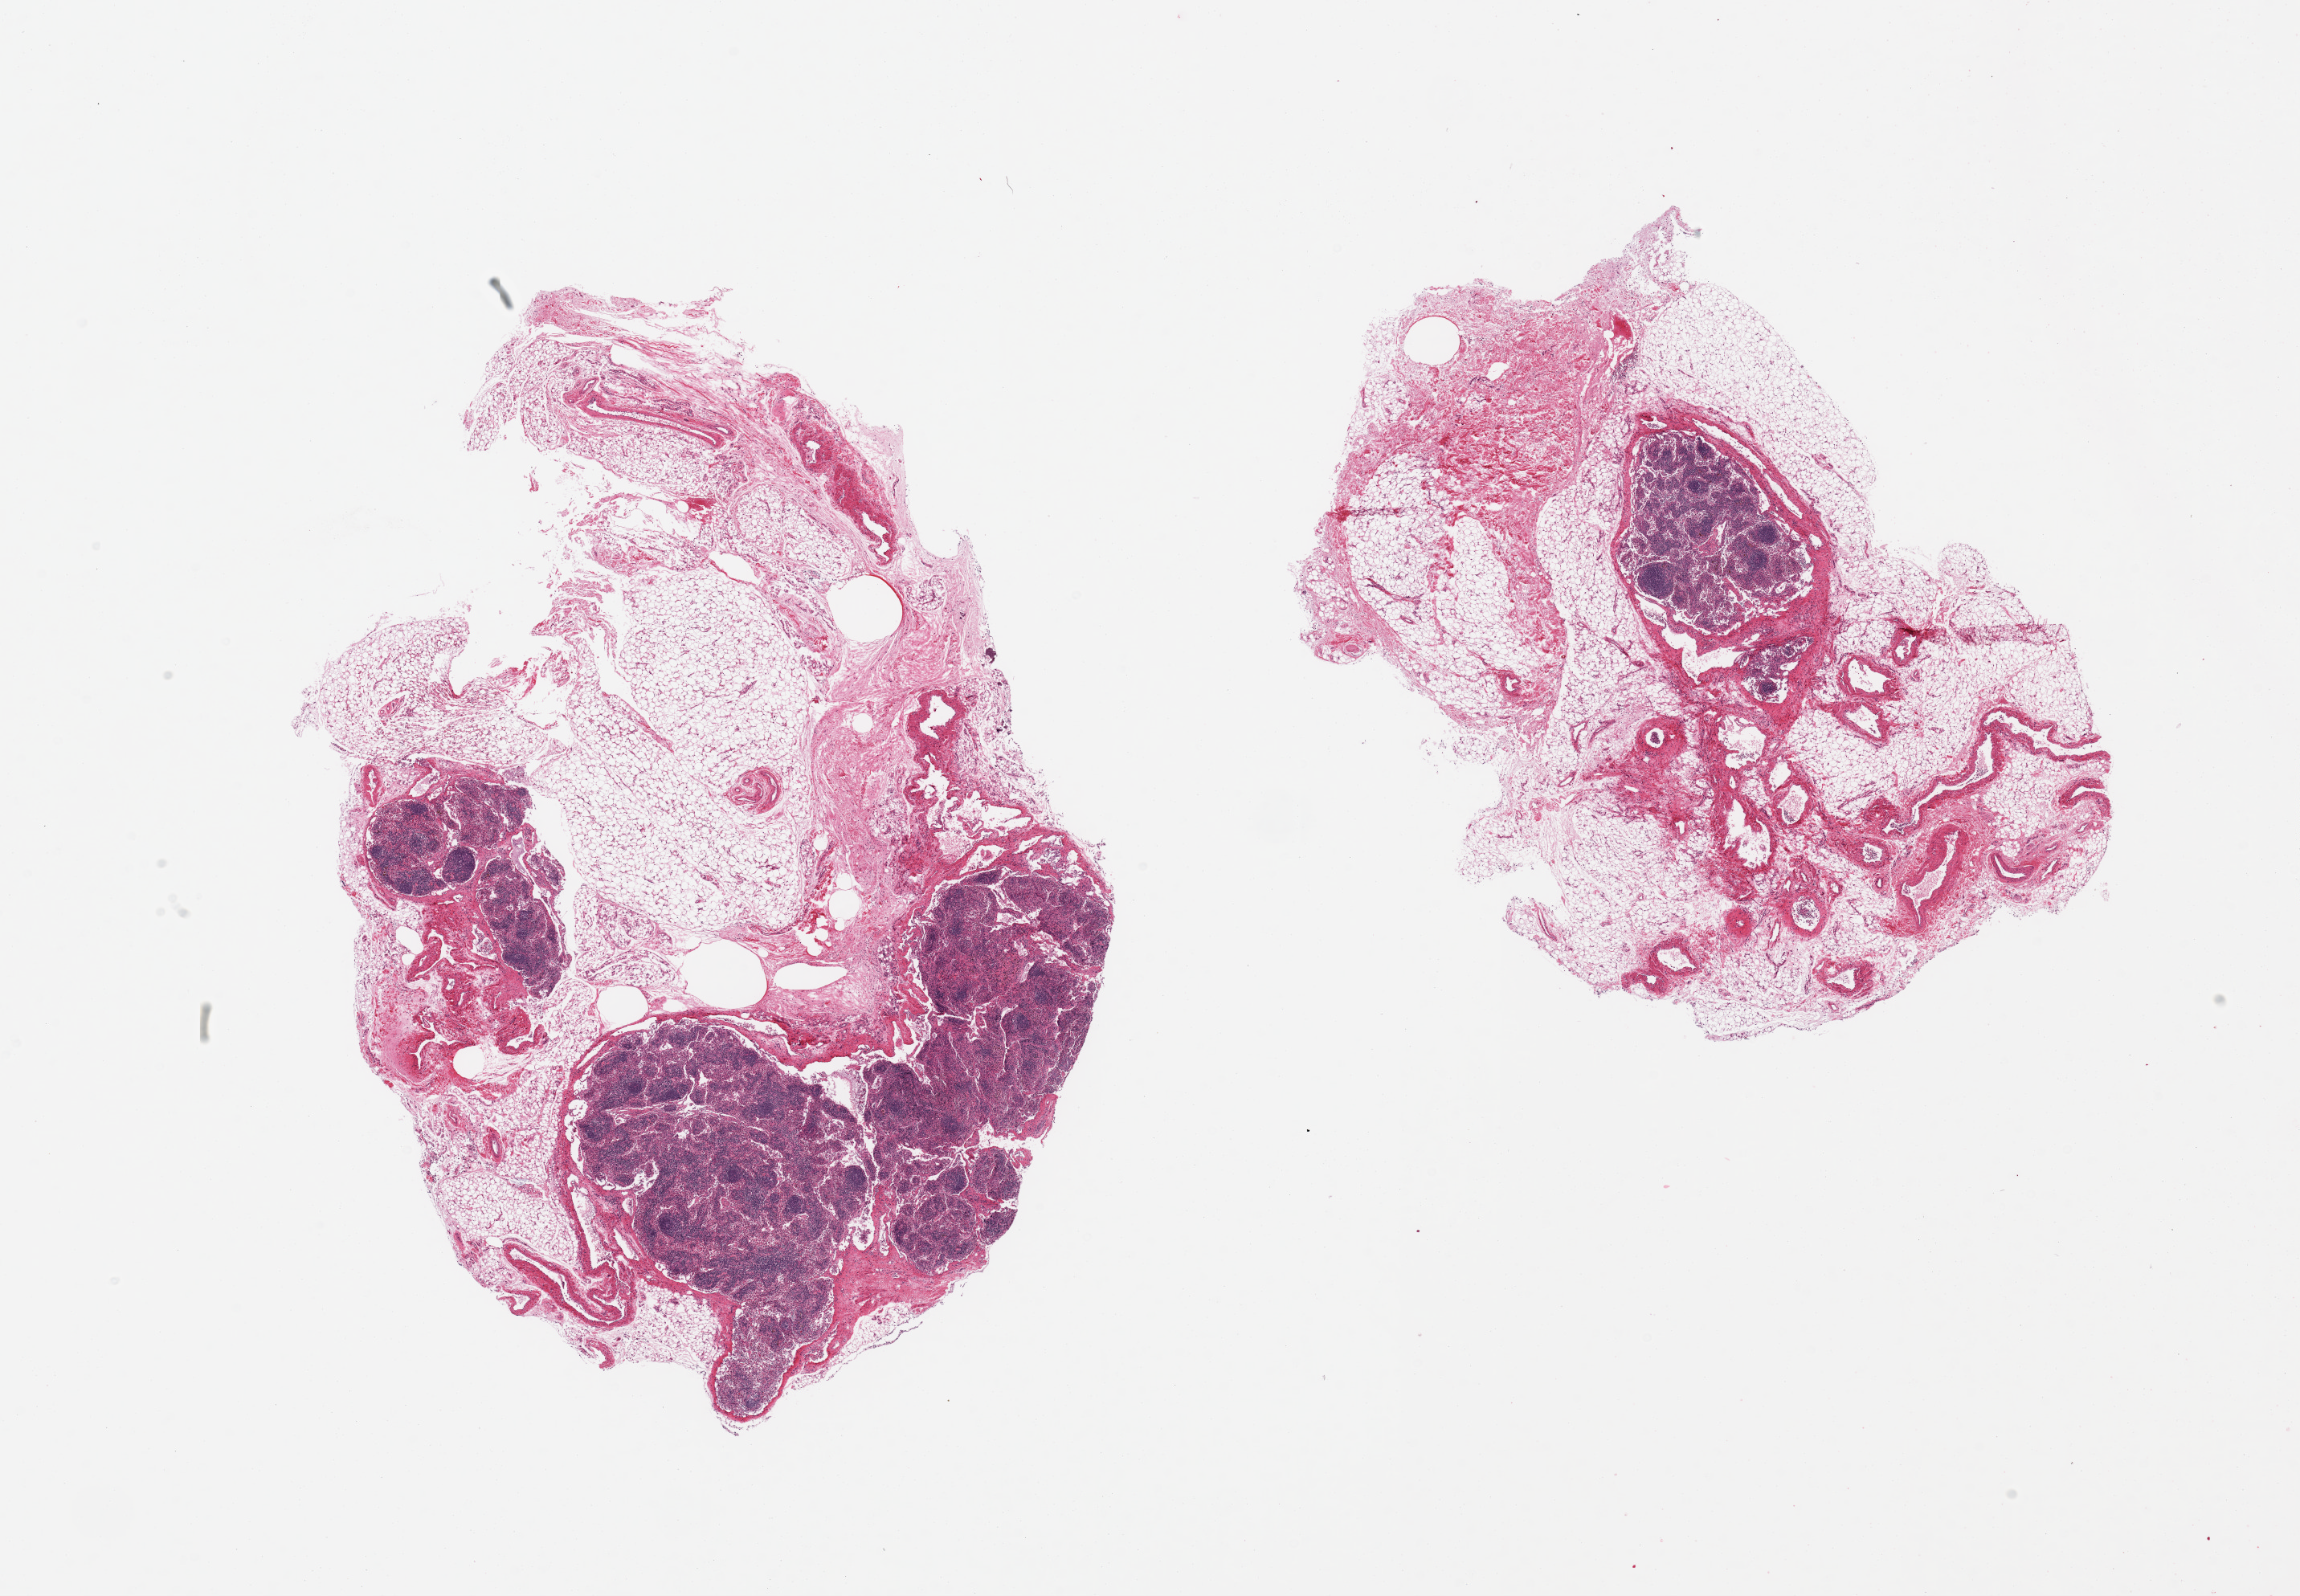
Whole-slide image, H&E stain, brightfield — shown as a low-resolution overview of the whole scanned area (about 22.6 x 15.7 mm, slide scanned at 20x), PAXgene-fixed paraffin-embedded (PFPE) section, section of thyroid (target tissue), donor tissue sample. Male donor.
• review note (as recorded): 2 pieces; lymphoid tissue and 50% and 75% fibrovascular tissue with fat; no target thyroid gland resent